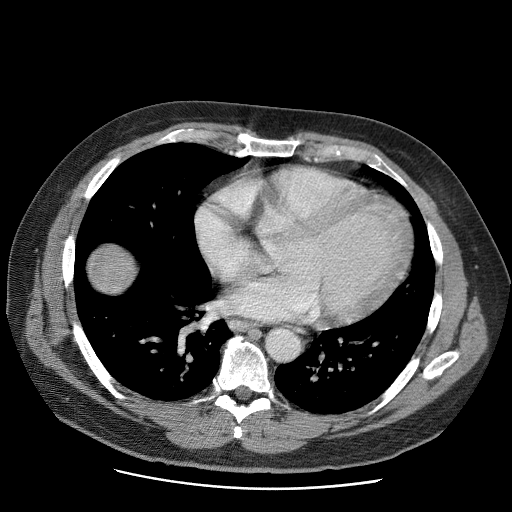
Contrast-enhanced abdominal CT (liver protocol), one axial slice; slice 70 of 81 in the series (ordered by position); reconstruction kernel STANDARD; 120 kVp; soft-tissue window (W 400 / L 40 HU); 2.5 mm slice thickness; 512 × 512 image matrix. From the clinical record (not read from this slice): diagnosis: hepatocellular carcinoma (patient treated with transarterial chemoembolisation; whether this scan precedes or follows treatment is not stated here); TNM stage (as recorded): Stage-IIIA; Child-Pugh class: A; tumour size: 5.5 cm.
Outlined on this slice (semi-automatically segmented with operator editing):
- liver parenchyma outside the tumour (the mass and vessels are separate outlines, so this box may not span the whole liver): bounding box <88,245,136,292> (left, top, right, bottom; pixels)